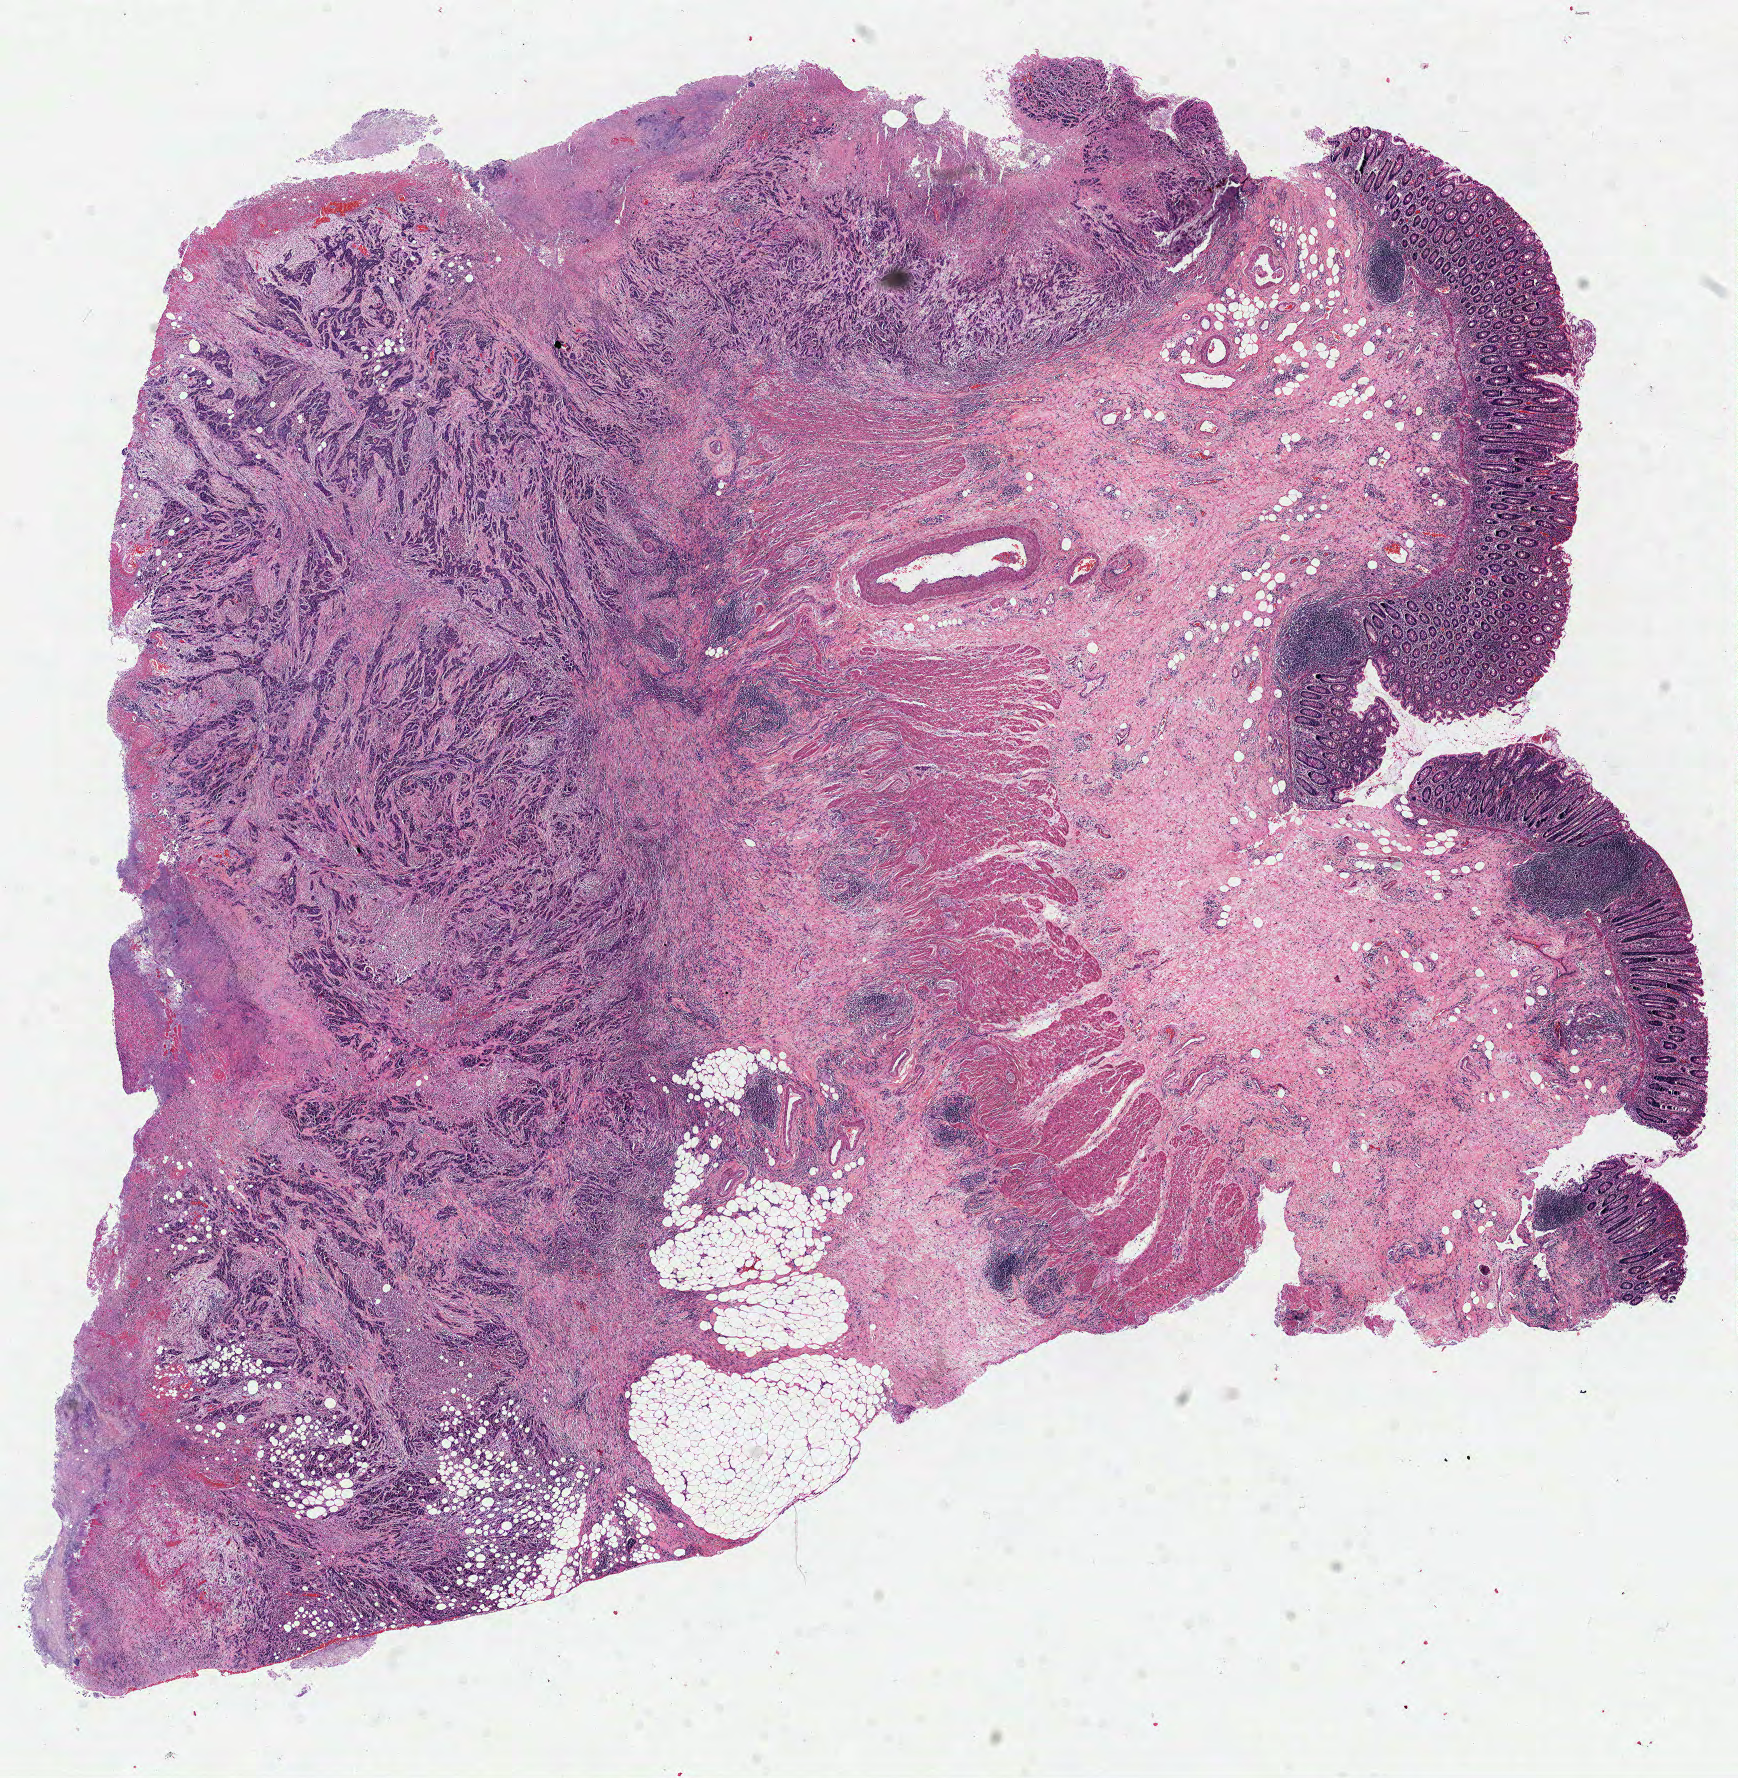
H&E whole-slide image, whole scanned area (about 14.0 x 14.3 mm, from a 40x scan) shown as a low-resolution overview, formalin-fixed paraffin-embedded (FFPE) diagnostic section, colon, primary tumour sample. Female patient; age at initial diagnosis 68 years.
• pathologic diagnosis: Adenocarcinoma, NOS (sigmoid colon)
• AJCC pathologic stage: IIA (7th edition)
• TNM: T3 N0 M0